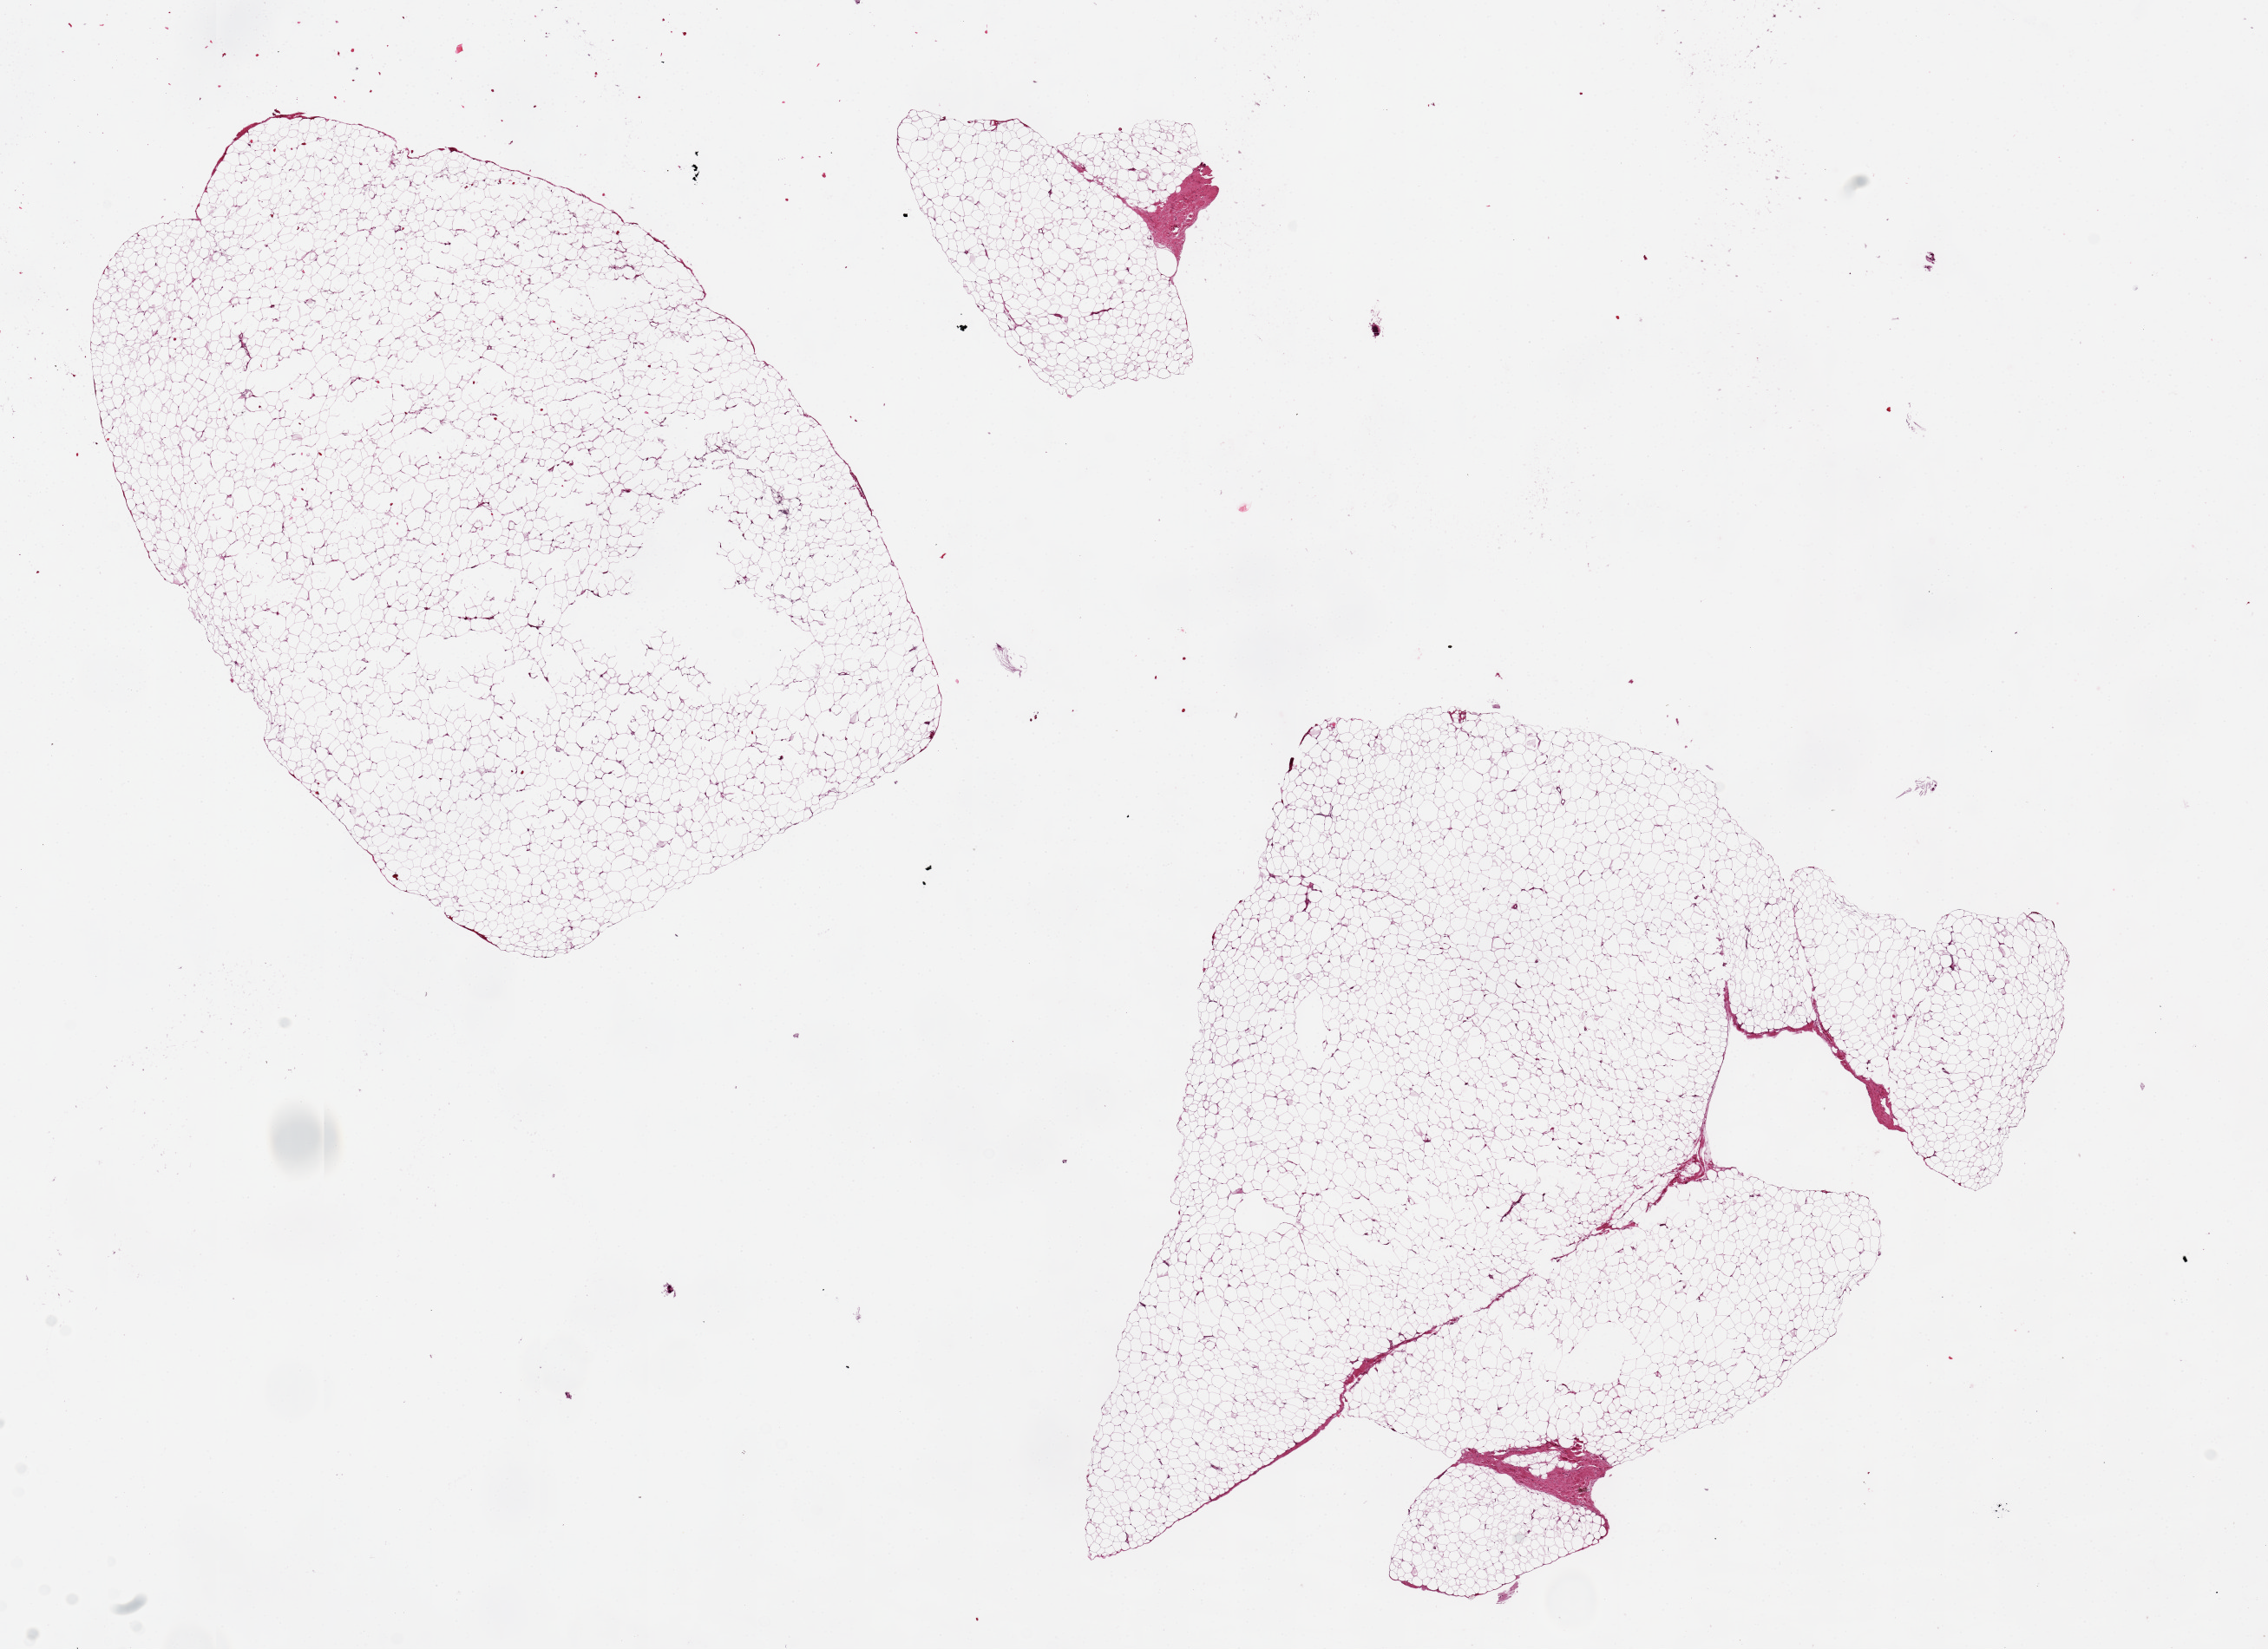
Hematoxylin and eosin (H&E) whole-slide image — a low-resolution overview of the entire scanned area, about 20.7 x 15.0 mm (slide scanned at 20x). PAXgene-fixed, paraffin-embedded tissue. Target tissue: adipose tissue. Tissue donor sample. Donor sex: female.
- reviewer comment on this tissue sample: 3 pieces, up to 10x7 mm; some central defects